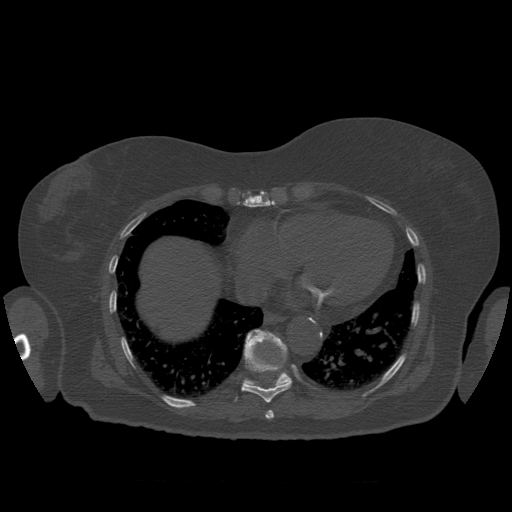
CT including the spine, one axial slice; reconstruction kernel STANDARD; 120 kVp; bone window (W 1800 / L 400 HU); 512 × 512 image matrix, field of view 404 × 404 mm. Patient age 81 years. From the clinical record (not read from this slice): primary cancer: renal.
Structures marked on this image (semi-automatic segmentation, software-assisted and operator-edited):
- T10 vertebra: bounding box (x1, y1, x2, y2) in pixels: (245, 330, 292, 389)
- T8 vertebra: (266, 410, 274, 419)
- T9 vertebra: (242, 333, 292, 403)